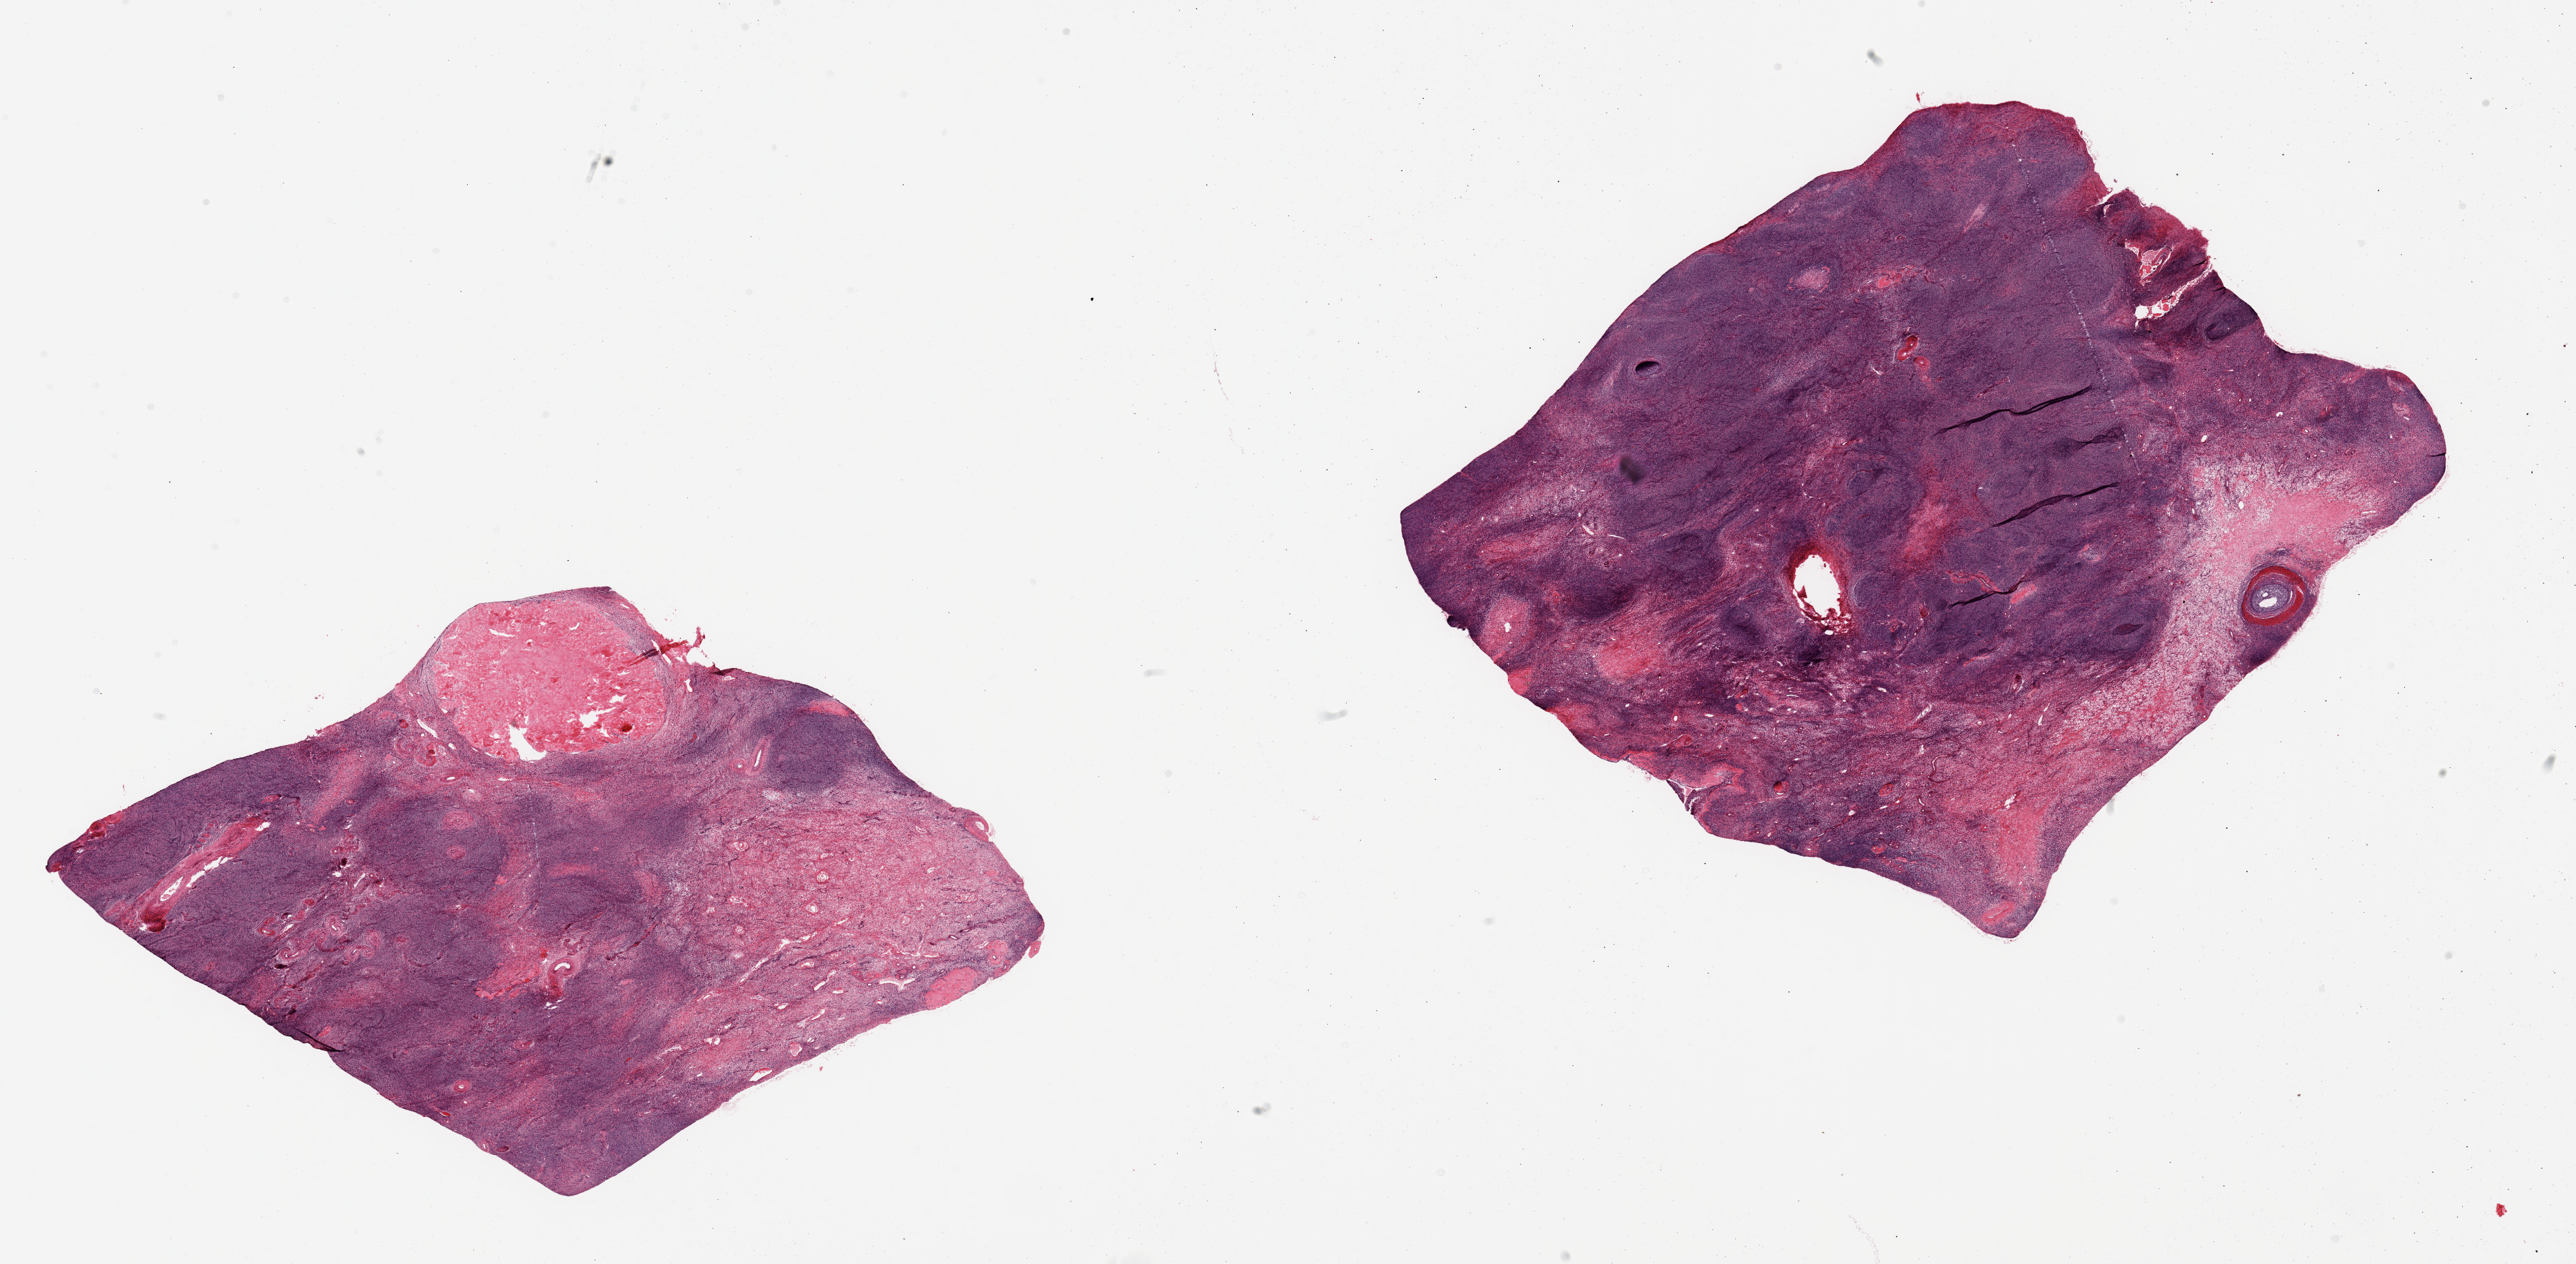
Whole-slide image, hematoxylin and eosin (H&E) stain — low-resolution overview of the scanned area, about 29.5 x 14.5 mm (slide scanned at 20x); PAXgene-fixed, paraffin-embedded tissue; target tissue: ovary; tissue donor sample.
Reviewer comment on this tissue sample: 2 pieces. No abnormalities.